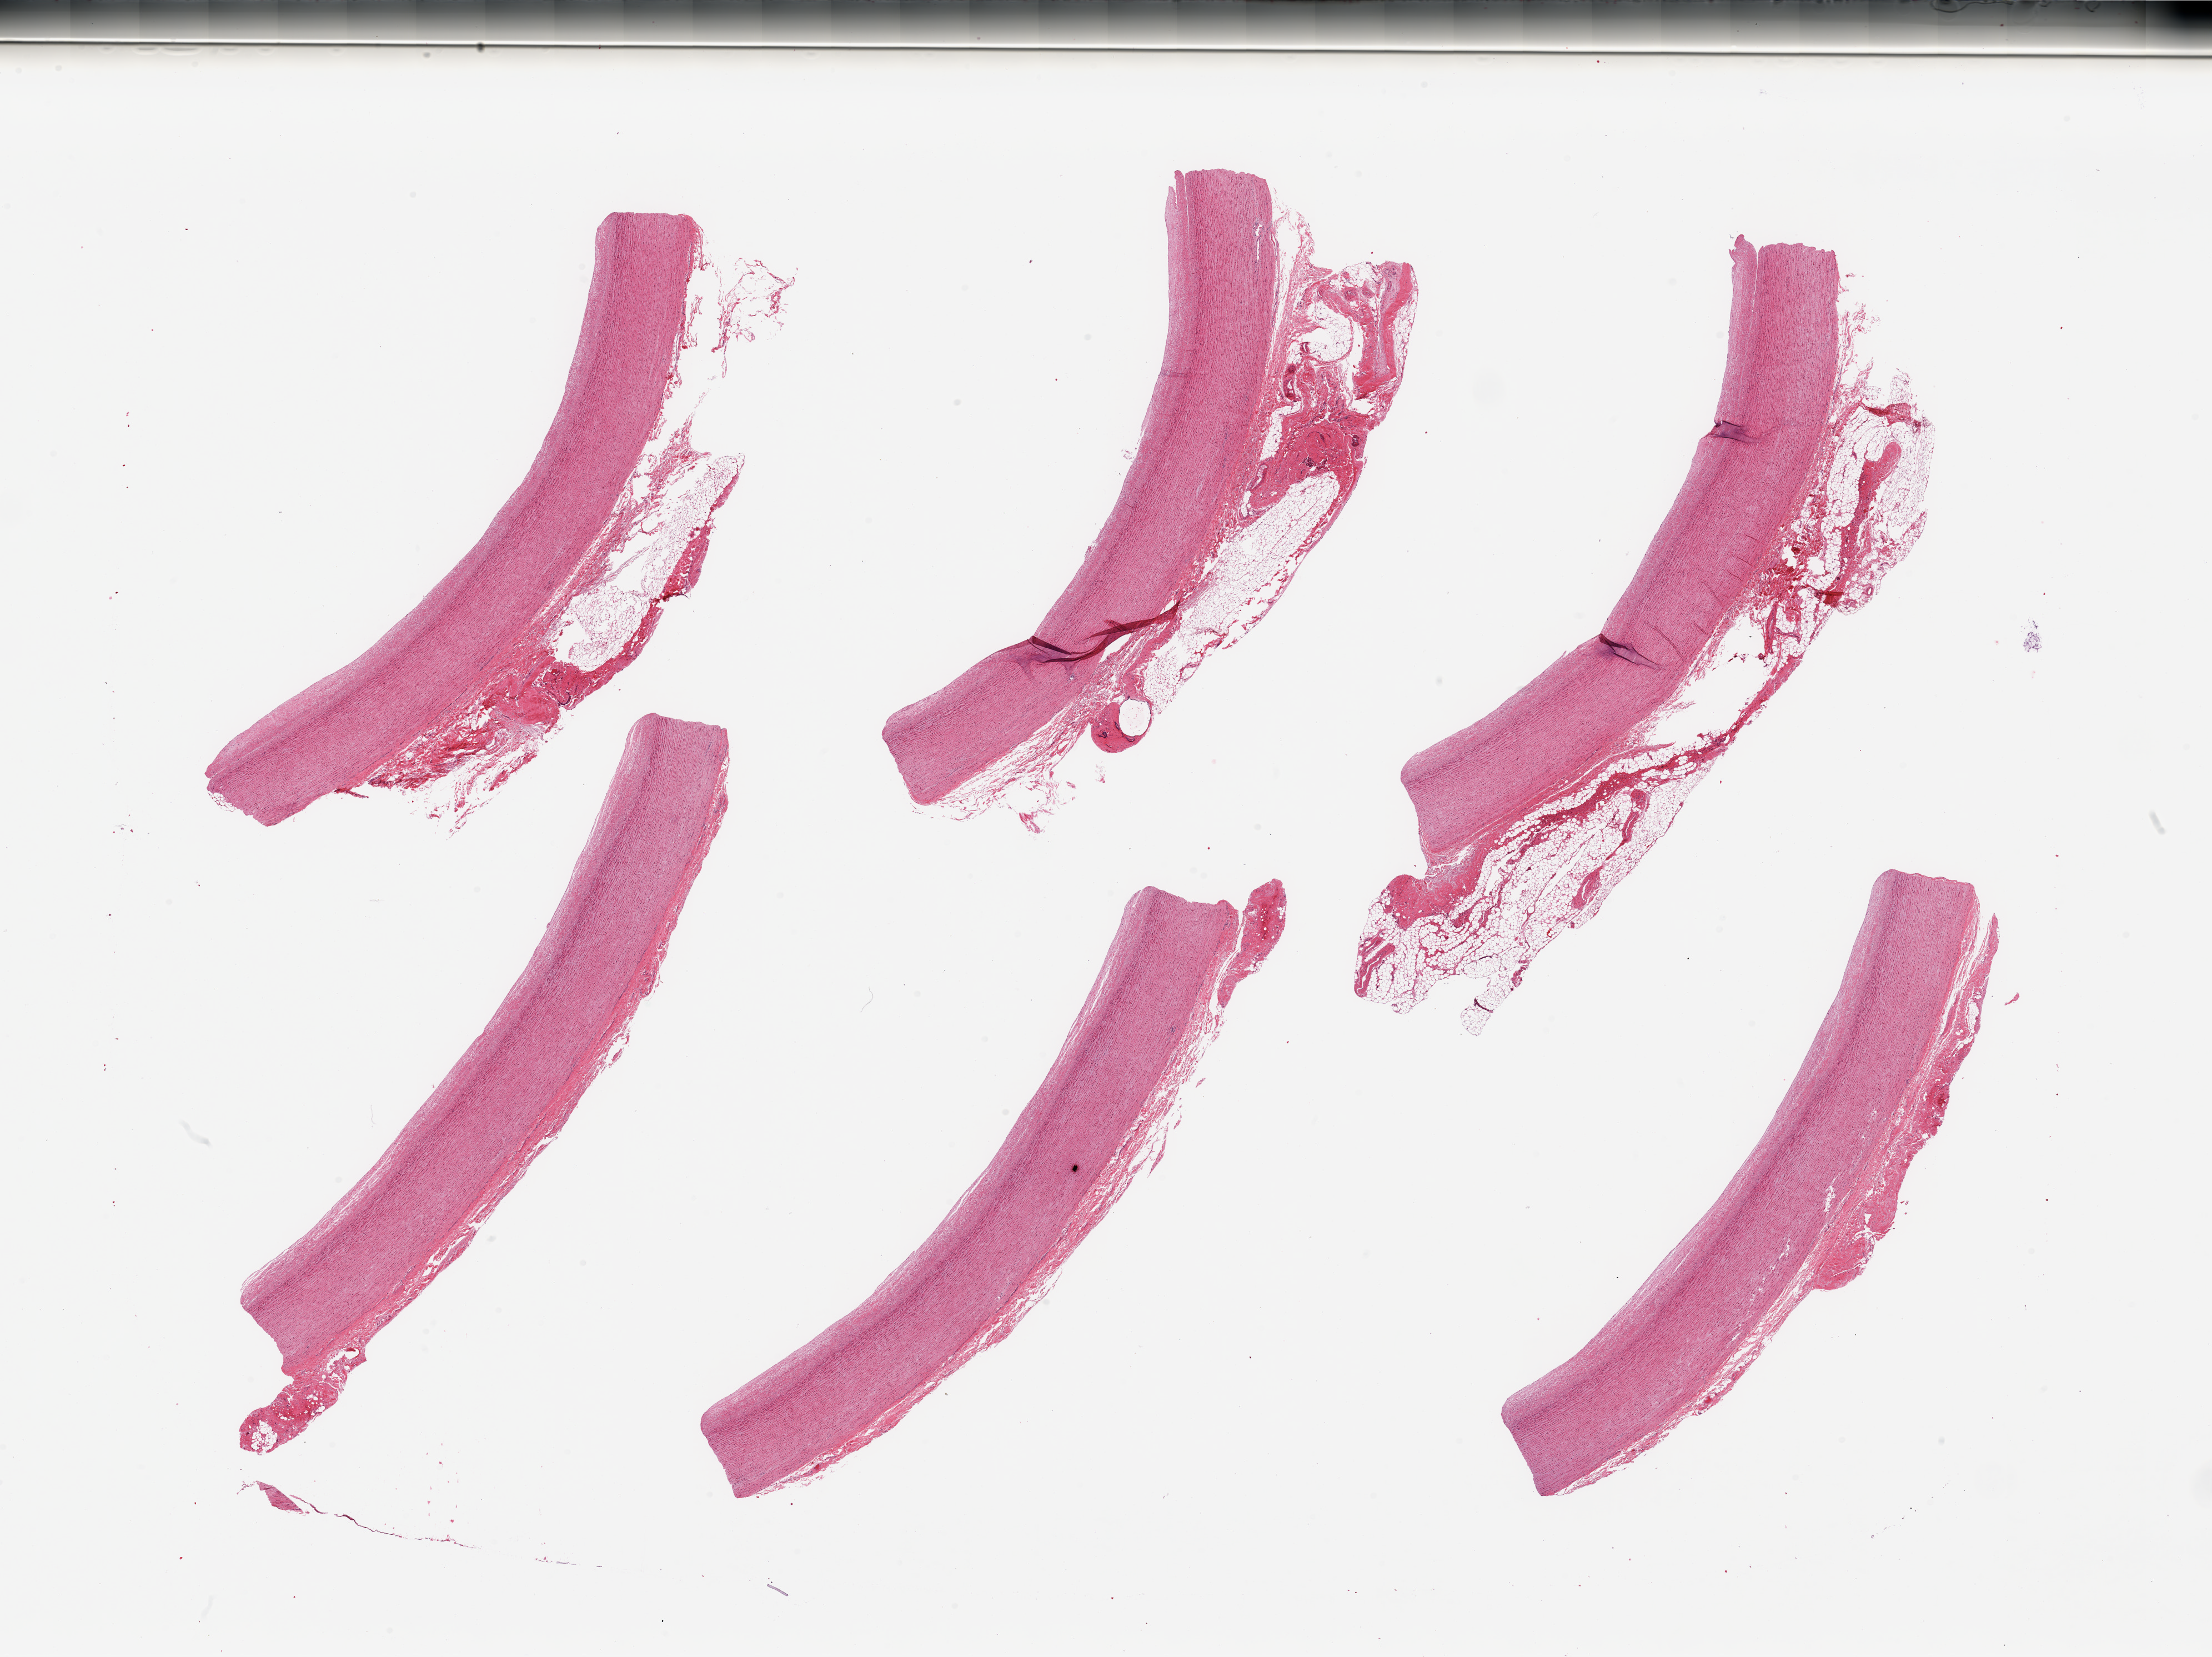
Digitized H&E-stained section, brightfield — shown as a low-resolution overview of the whole scanned area (about 31.5 x 23.6 mm). PAXgene-fixed, paraffin-embedded tissue. Target tissue: aorta. Donor tissue sample. Male donor.
- pathologist's review note for this sample: 6 pieces; slight fibrous intimal thickening; fatty adventitia up to 1.7mm thick